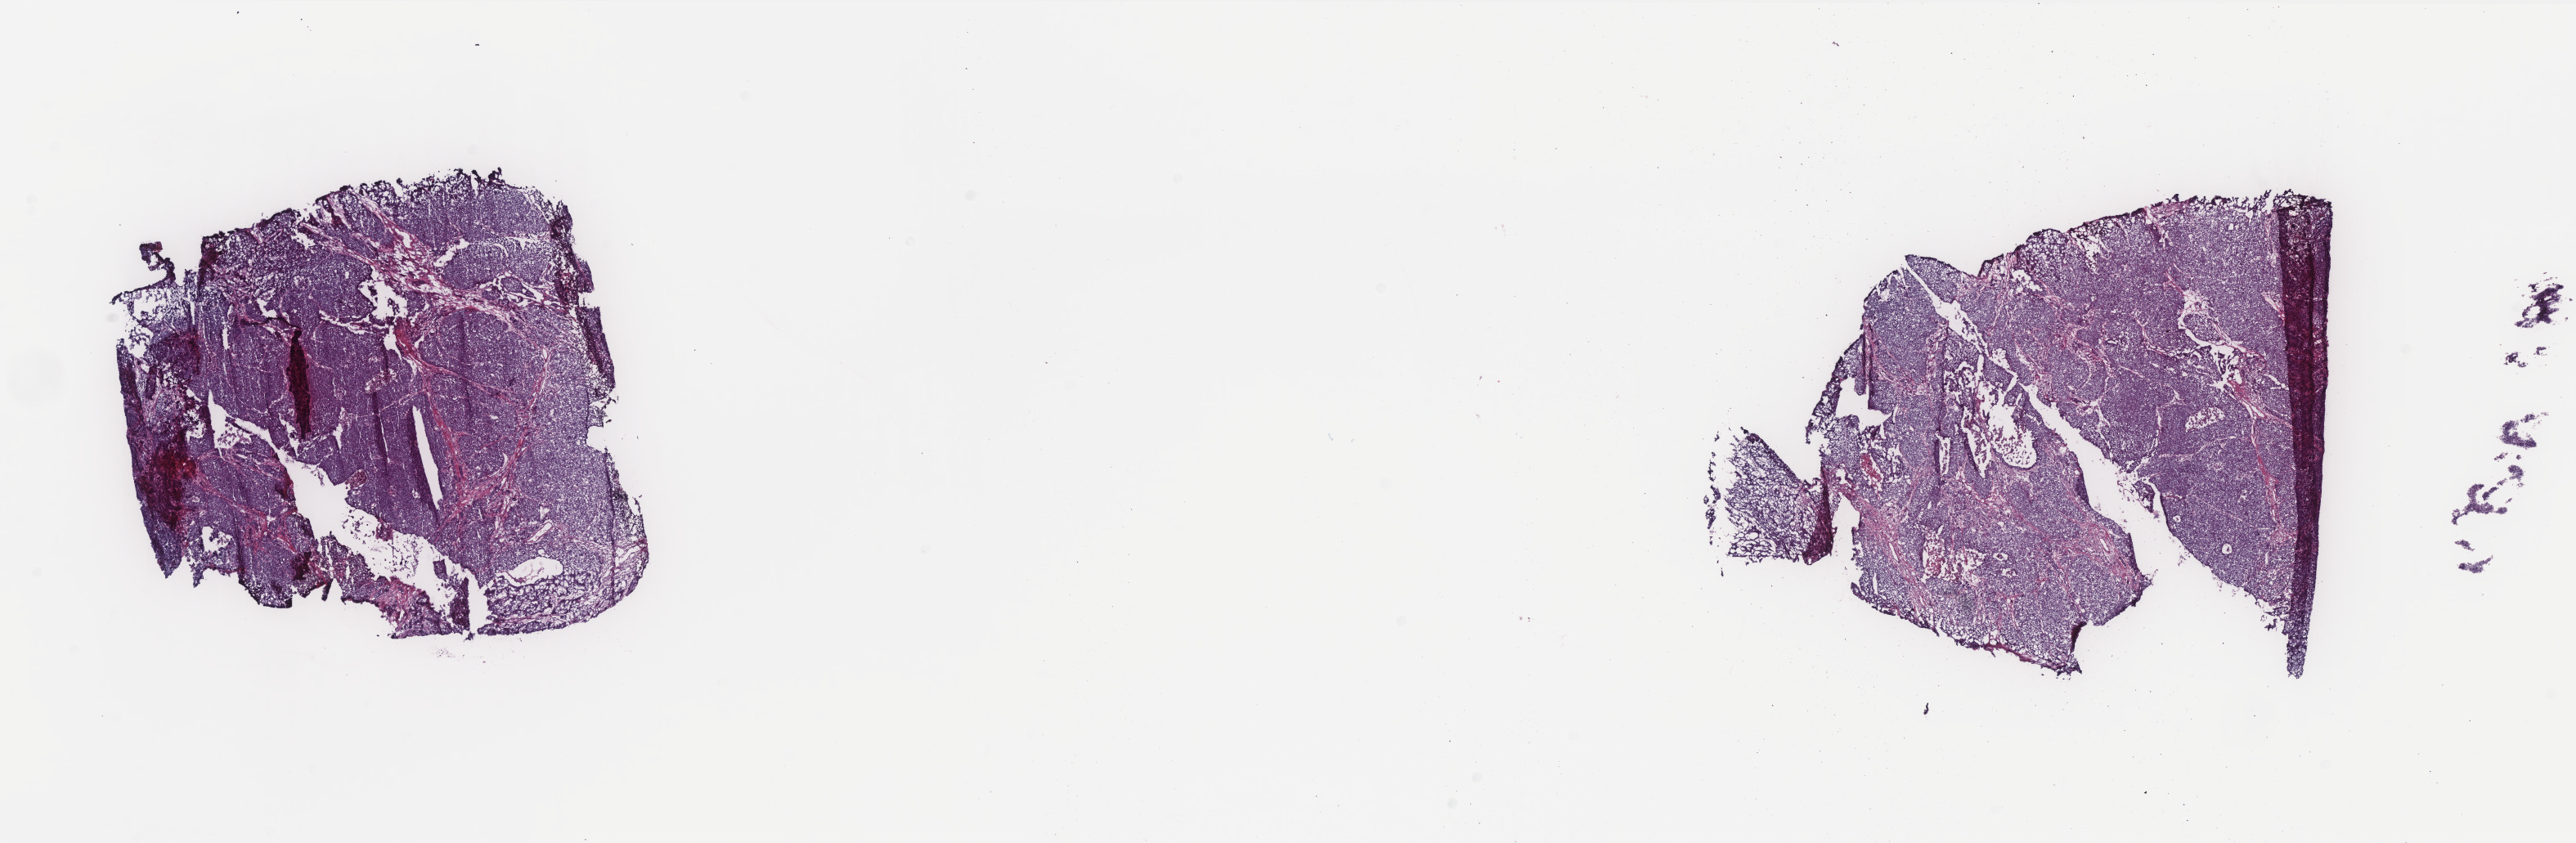
Whole-slide histology image, H&E, a low-resolution overview of the entire scanned area, about 25.3 x 8.3 mm, frozen section from the top of the tissue portion, primary tumour sample from the colon. Male patient. Slide review estimates, as recorded: tumour cells 95%, tumour nuclei 95%, normal cells 0%, stromal cells 0%, necrosis 5%. Infiltration values recorded for this section: lymphocyte infiltration 0%, monocyte infiltration 0%, neutrophil infiltration 0%.
AJCC pathologic stage: IIIC. TNM: T3 N2 M0. Diagnosis: Adenocarcinoma, NOS. Lymph nodes positive (case pathology): 4 of 17 examined.